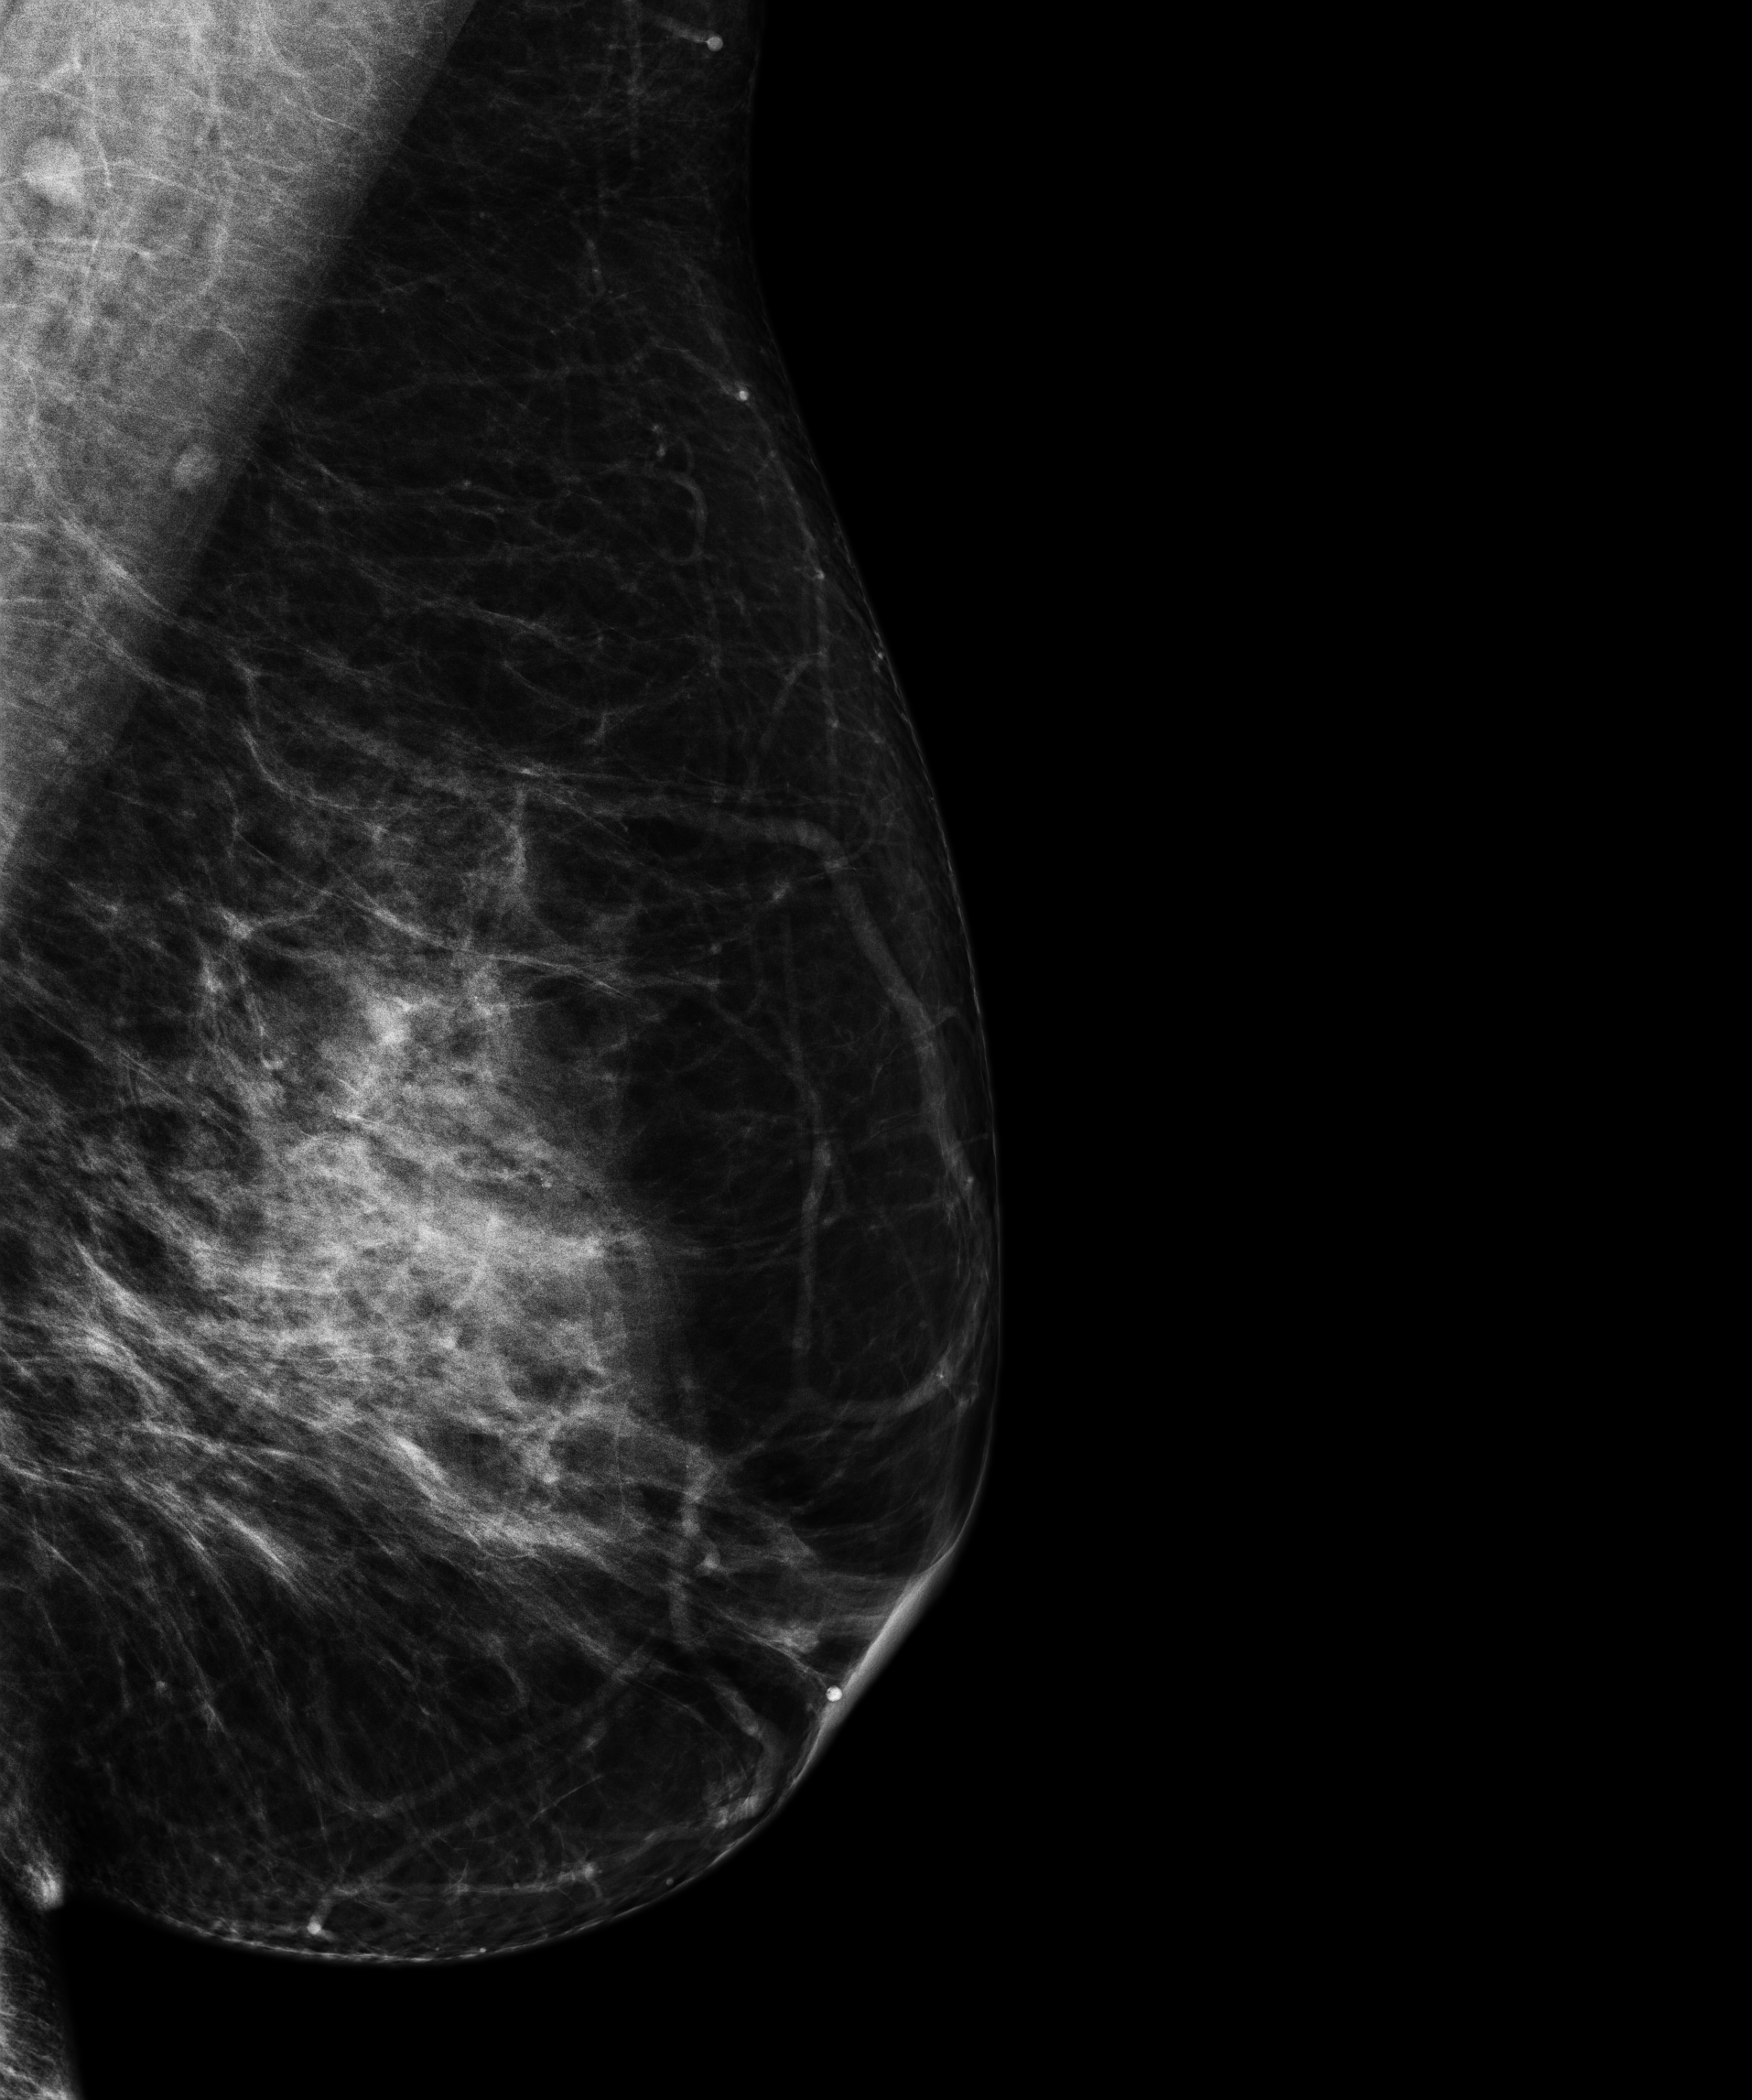
Annual screening mammography examination; system: Senographe Pristina. Patient: female, 48 years.
Image type: full-field digital mammogram. Breast: left. Projection: MLO view.